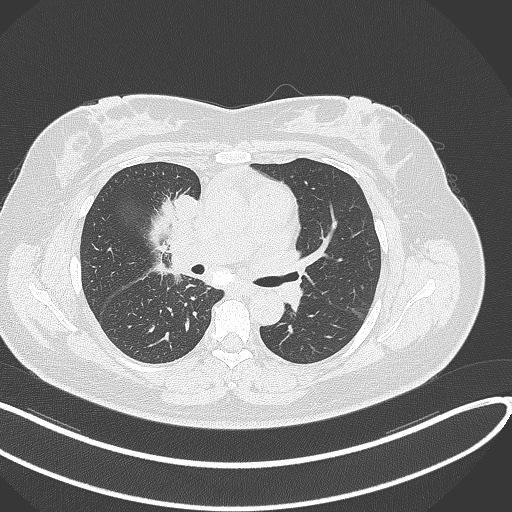
Chest CT, one axial slice; position 155 of 303 along the scan axis; 120 kVp; lung window (W 1500 / L -600 HU); 1 mm slice thickness; 512 × 512 image matrix, field of view 400 × 400 mm. Female patient, age 46 years. Case-level facts recorded for this patient, not image findings: clinical TNM (as recorded): T2a N1 M0.
Structures marked on this image (rectangle marked by the reading radiologist):
- lung tumour (recorded histology: adenocarcinoma): bounding box [x1, y1, x2, y2] px = [169, 189, 200, 223]